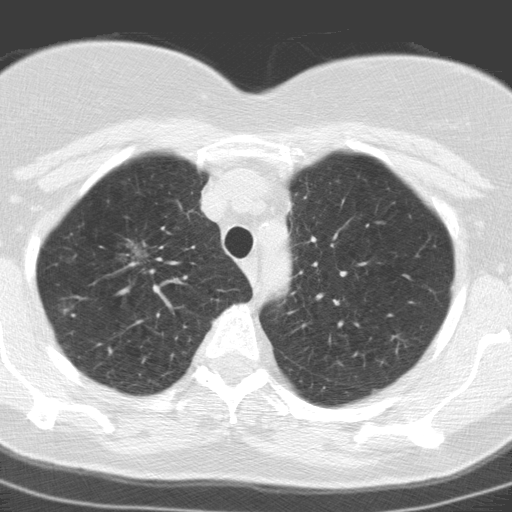
Low-dose screening chest CT, axial slice. Baseline annual screen. Lung window (W 1500 / L -600 HU). 3.2 mm slice thickness. Slice 32 of 165 in the series. Female, age 60 years at enrolment. Former smoker at enrolment.
Lesion marked by an expert reader, bounding box <105,228,159,275> (left, top, right, bottom; pixels). Screening reader's record for this exam: no non-calcified nodule ≥4 mm recorded. Lung cancer was diagnosed 447 days after this screen (after the second annual screen): adenocarcinoma, NOS, right upper lobe, moderately differentiated (G2), stage IA (AJCC 6th edition), 23 mm at pathology.